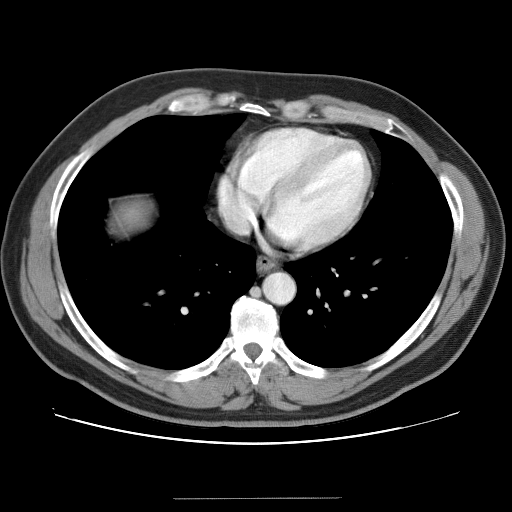
Contrast-enhanced abdominal CT (liver protocol), one axial slice. Position 38 of 40 along the scan axis. Soft-tissue window (W 400 / L 40 HU). 5 mm slice thickness. 512 × 512 image matrix, field of view 380 × 380 mm. Case-level facts recorded for this patient, not image findings: diagnosis: hepatocellular carcinoma (patient treated with transarterial chemoembolisation; whether this scan precedes or follows treatment is not stated here); TNM stage (as recorded): Stage-IVA; Child-Pugh class: B; tumour nodularity: multinodular.
Outlined on this slice (semi-automatic segmentation, software-assisted and operator-edited):
- liver parenchyma outside the tumour (the mass and vessels are separate outlines, so this box may not span the whole liver): bounding box (x1, y1, x2, y2) in pixels: (114, 202, 148, 230)